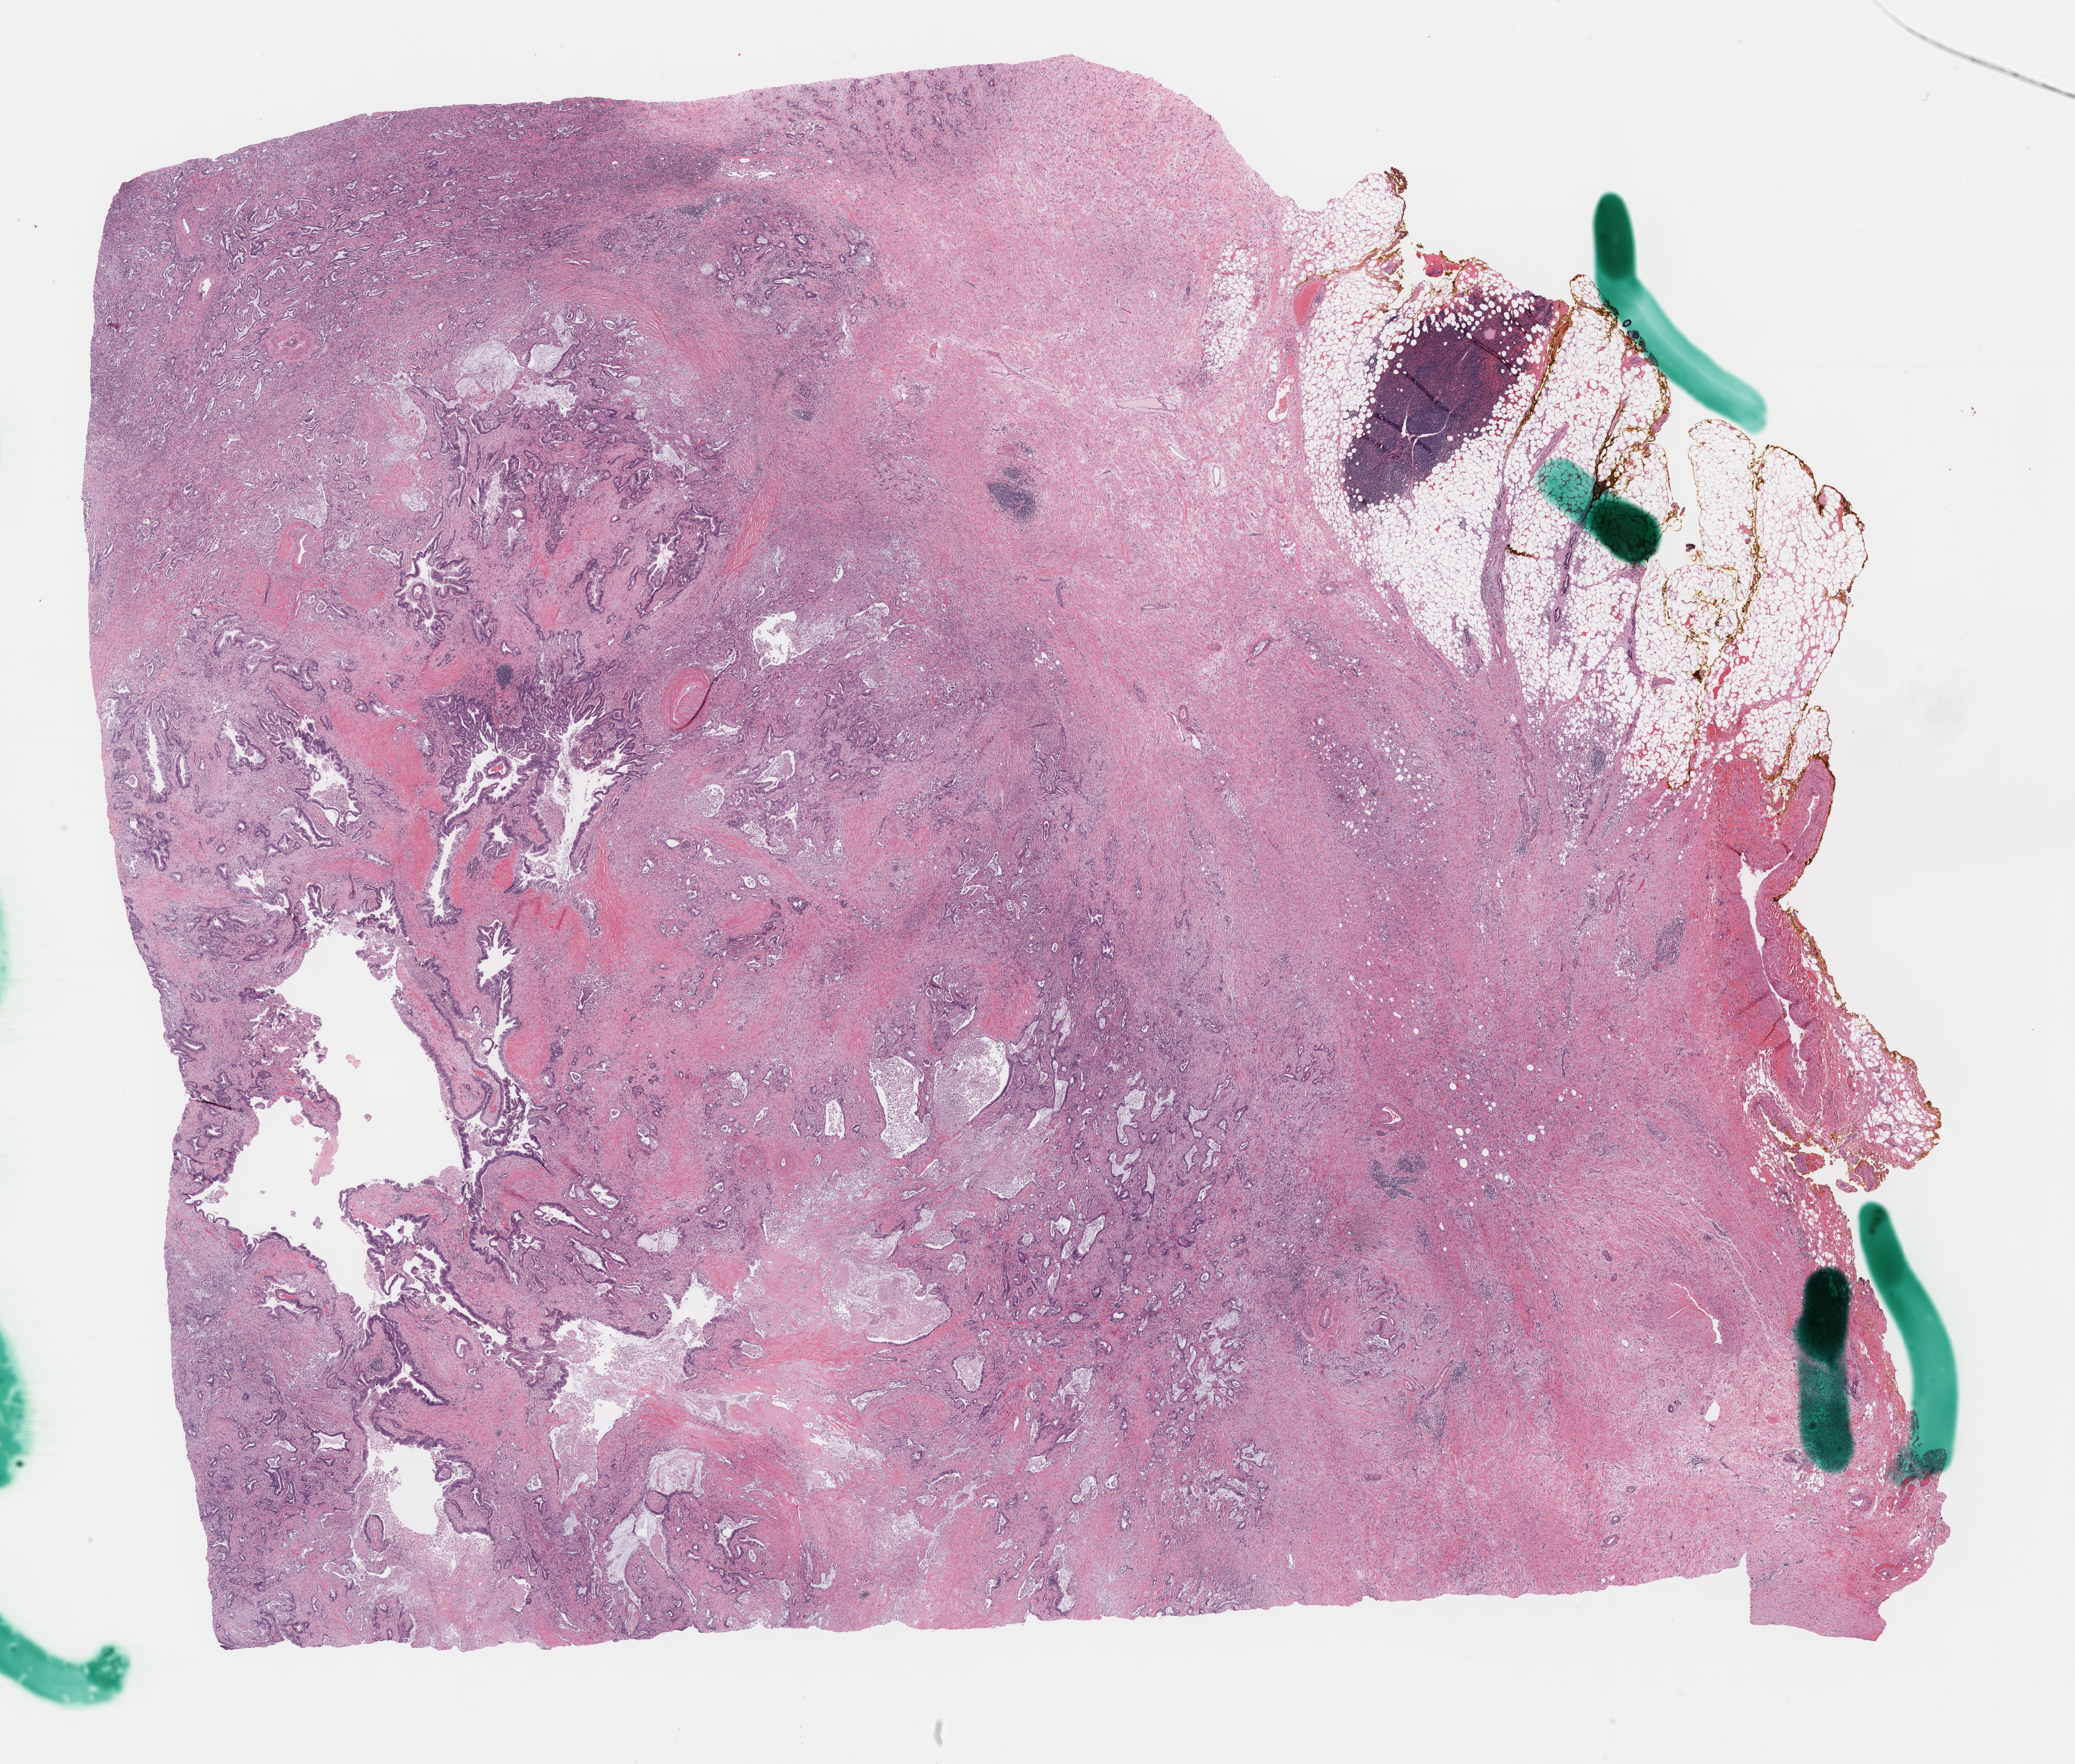
Whole-slide histology image, H&E — whole scanned area (about 24.2 x 20.5 mm) shown as a low-resolution overview; formalin-fixed paraffin-embedded (FFPE) diagnostic section; sample: primary tumour, pancreas. Female, age 84 years at initial diagnosis. Histologic grade: G2 (moderately differentiated).
- histologic diagnosis: Infiltrating duct carcinoma, NOS (head of pancreas)
- AJCC pathologic stage: IIB